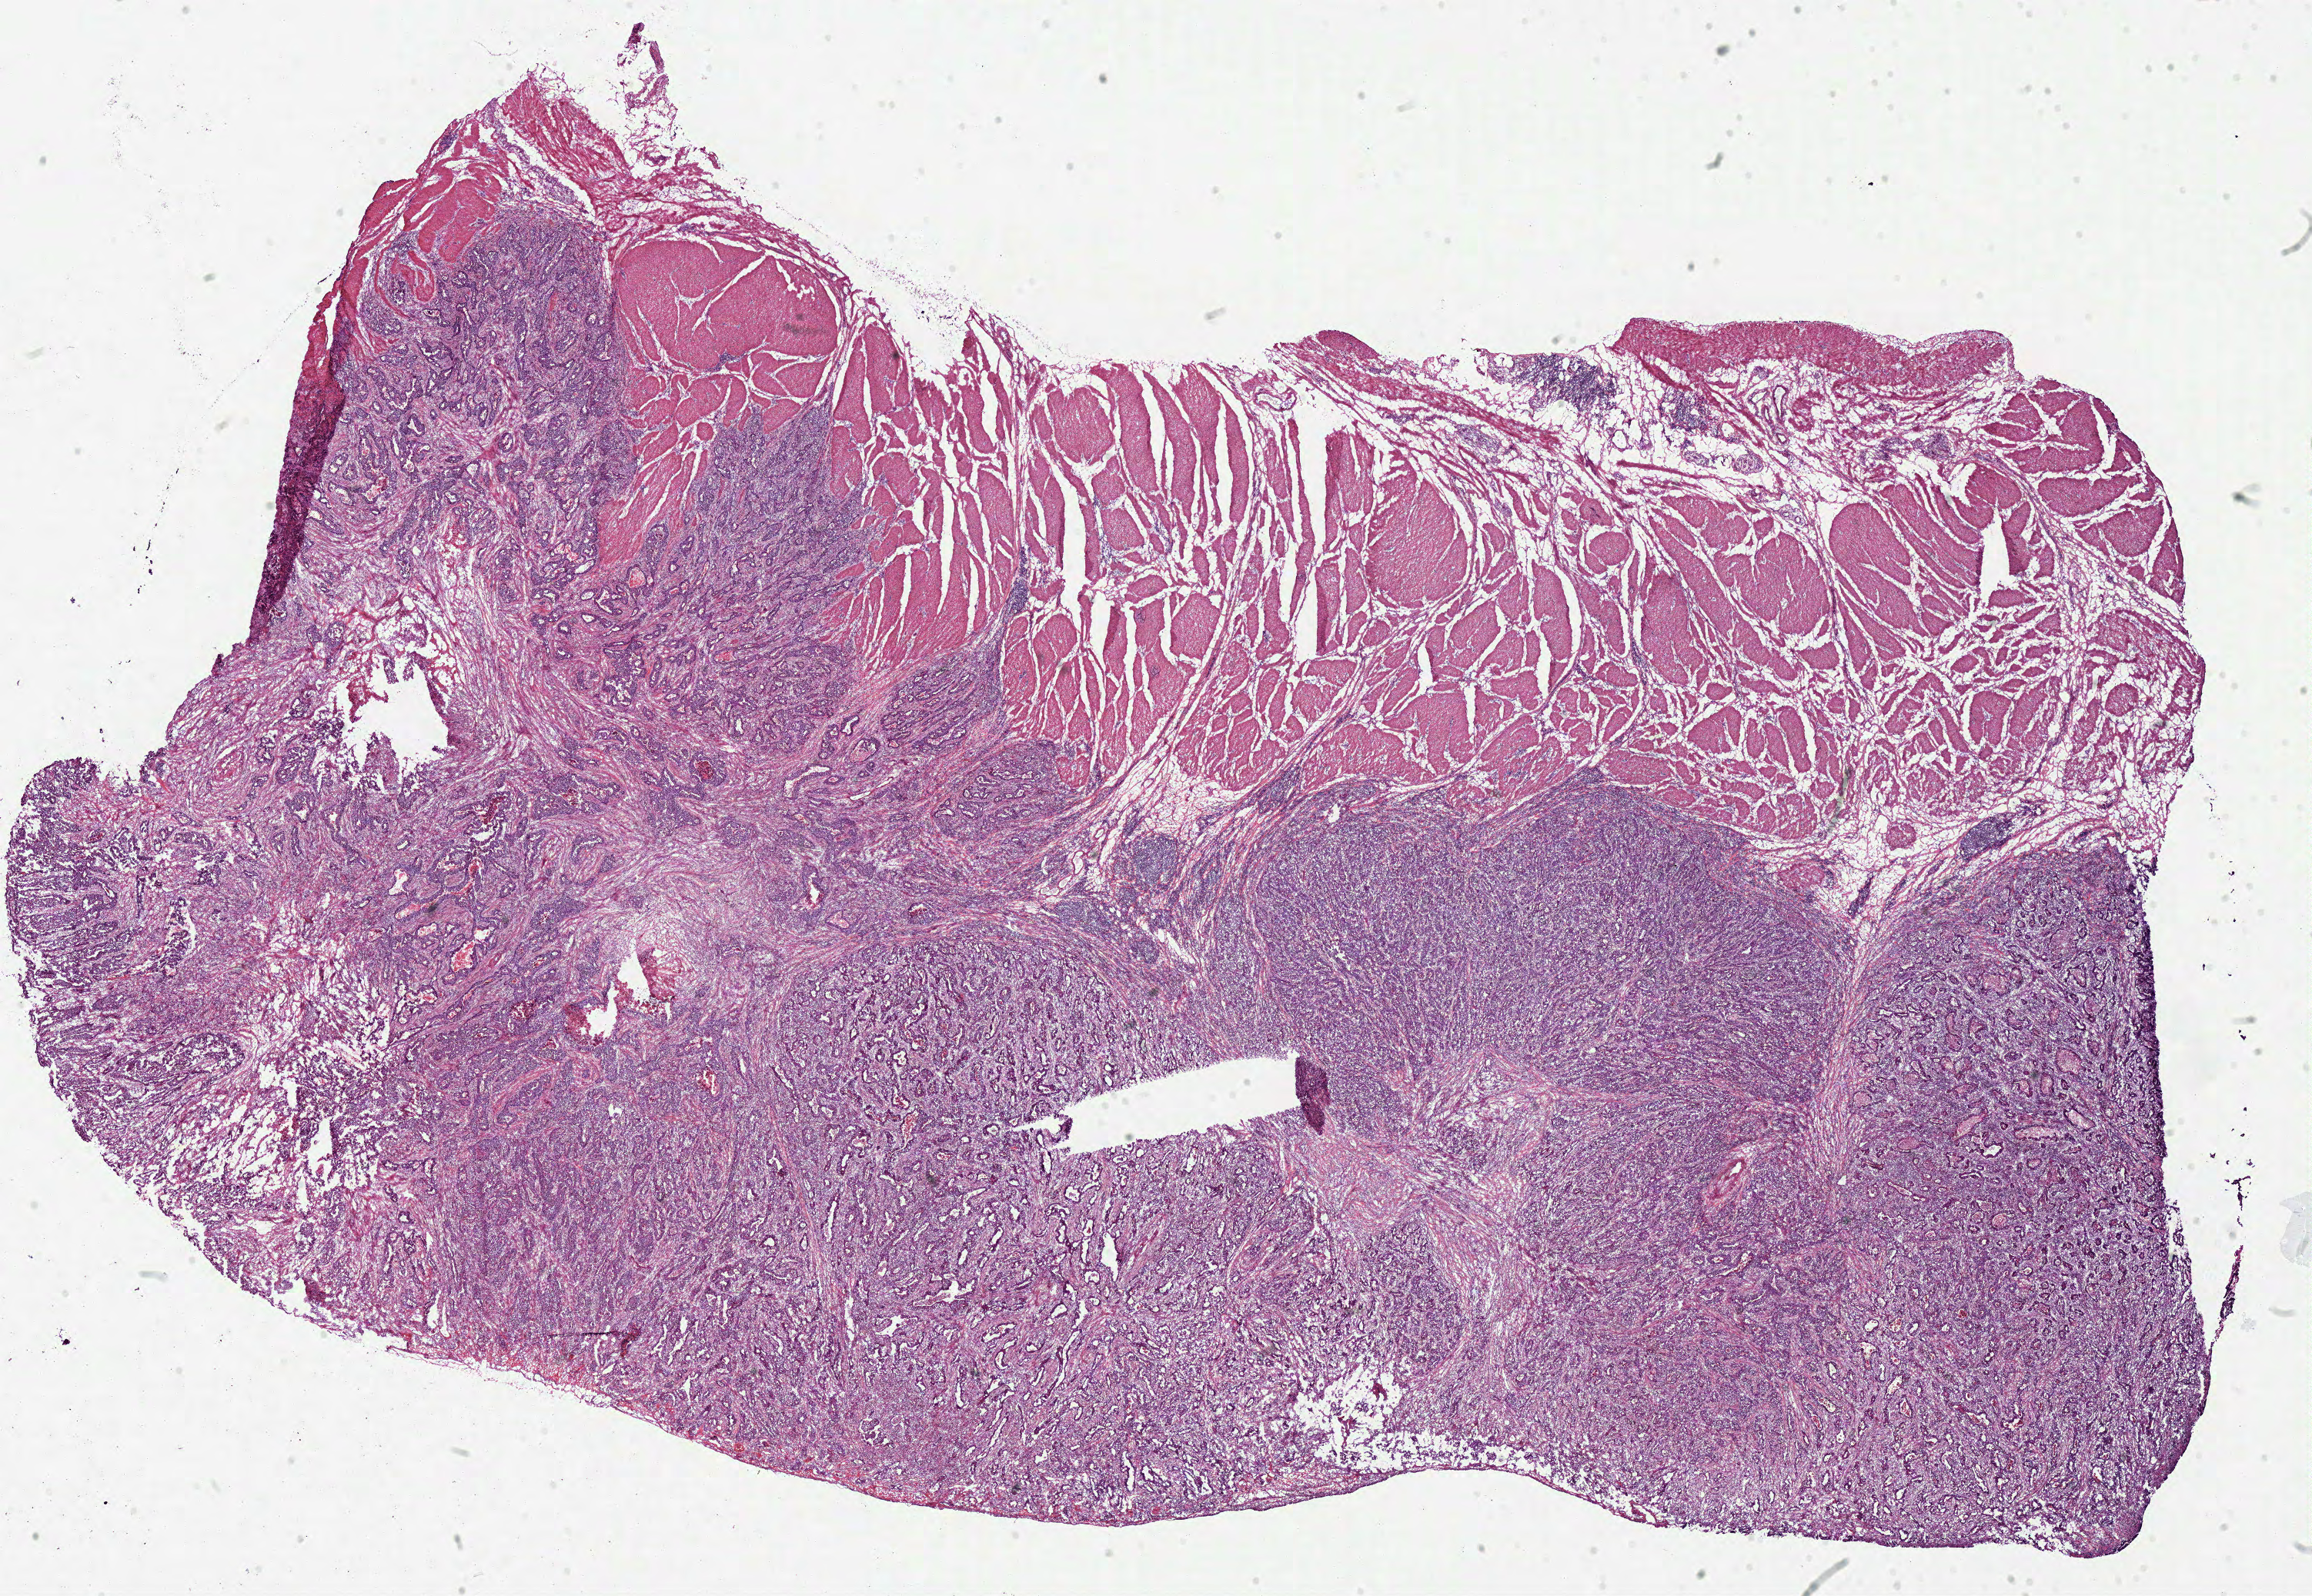
H&E-stained whole-slide image — low-resolution overview of the scanned area, about 23.7 x 16.3 mm (acquisition: 40x scan). Frozen section from the top of the tissue portion. Stomach, primary tumour sample. Male patient; age at initial diagnosis 67 years. Histologic grade: G2 (moderately differentiated). Composition of this section per pathologist review: tumour cells 60%, tumour nuclei 75%, normal cells 0%, stromal cells 30%, necrosis 10%.
Lymph nodes positive (case pathology): 0 of 1 examined. AJCC pathologic stage: IIB (7th edition). Pathologic diagnosis: Adenocarcinoma, NOS (body of stomach). TNM: T4a N0 M0.